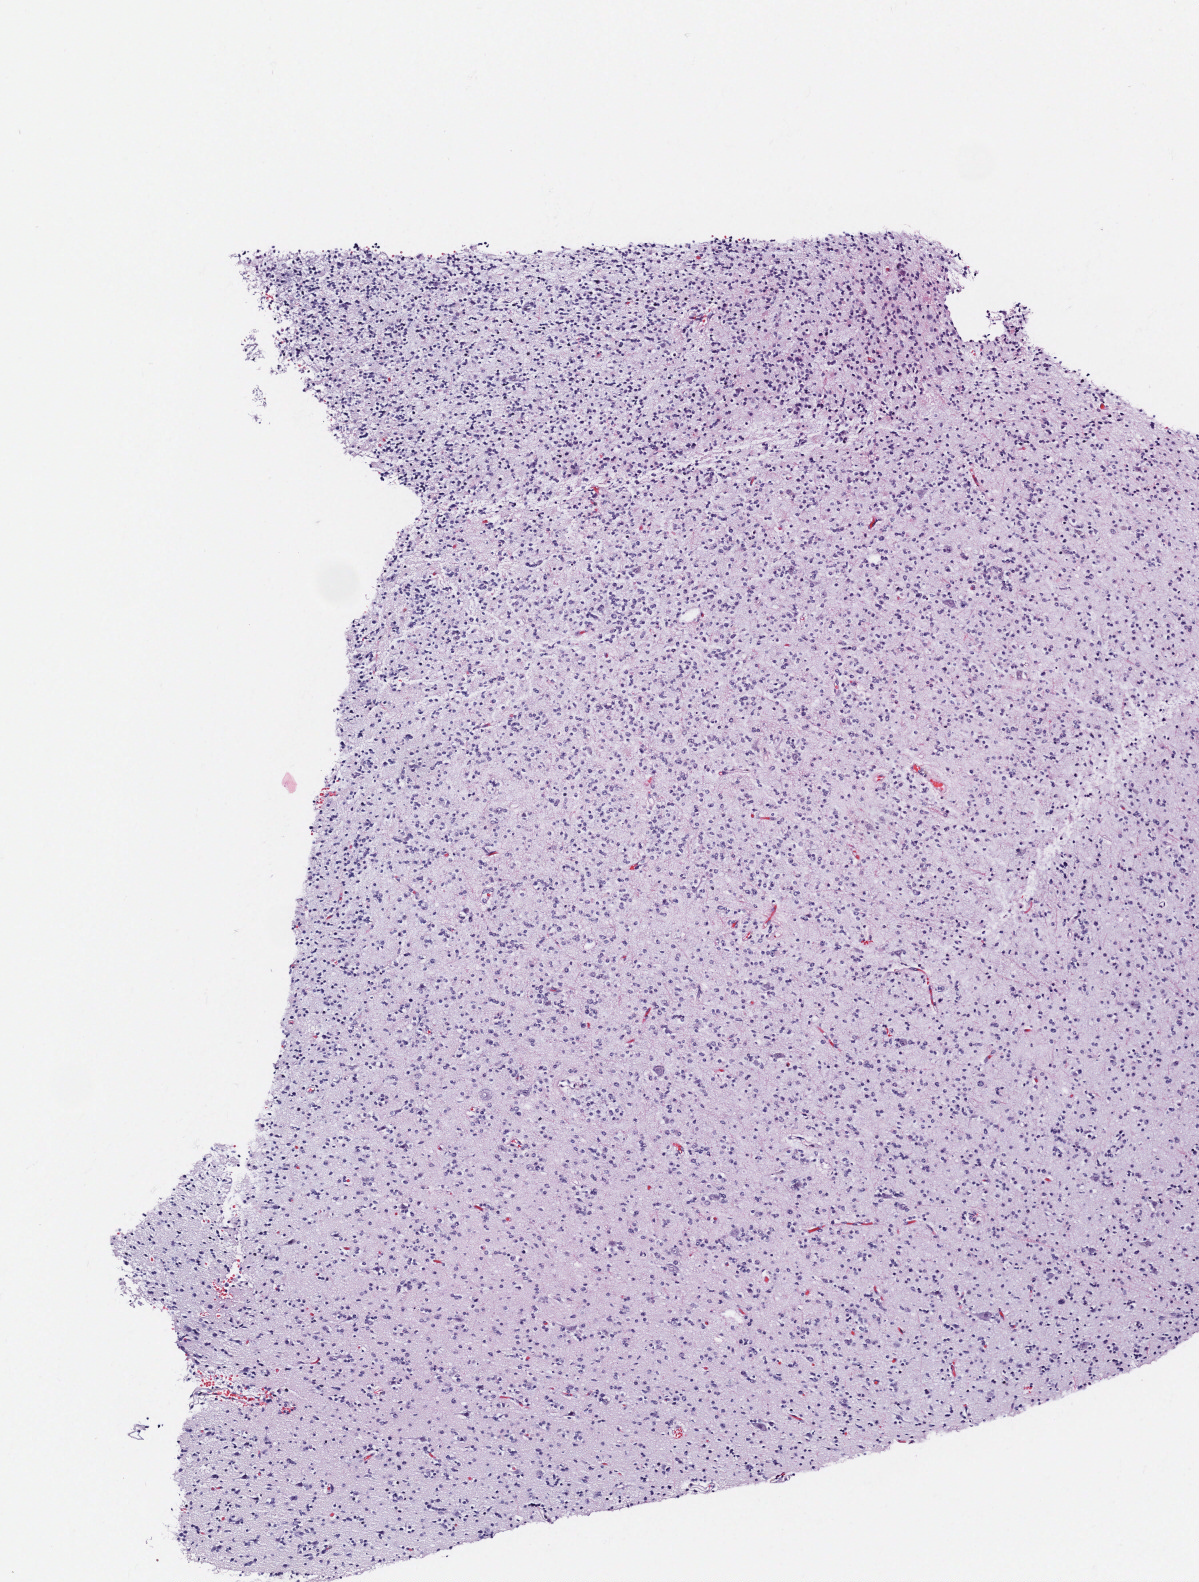
Digitized H&E-stained tissue section (whole slide) — low-resolution overview of the scanned area, about 2.4 x 3.2 mm (acquisition: 40x scan); formalin-fixed paraffin-embedded (FFPE) diagnostic section; primary tumour sample from the brain. Female, age 29 years at initial diagnosis. Histologic grade: G2 (moderately differentiated).
- pathologic diagnosis: Mixed glioma (cerebrum)